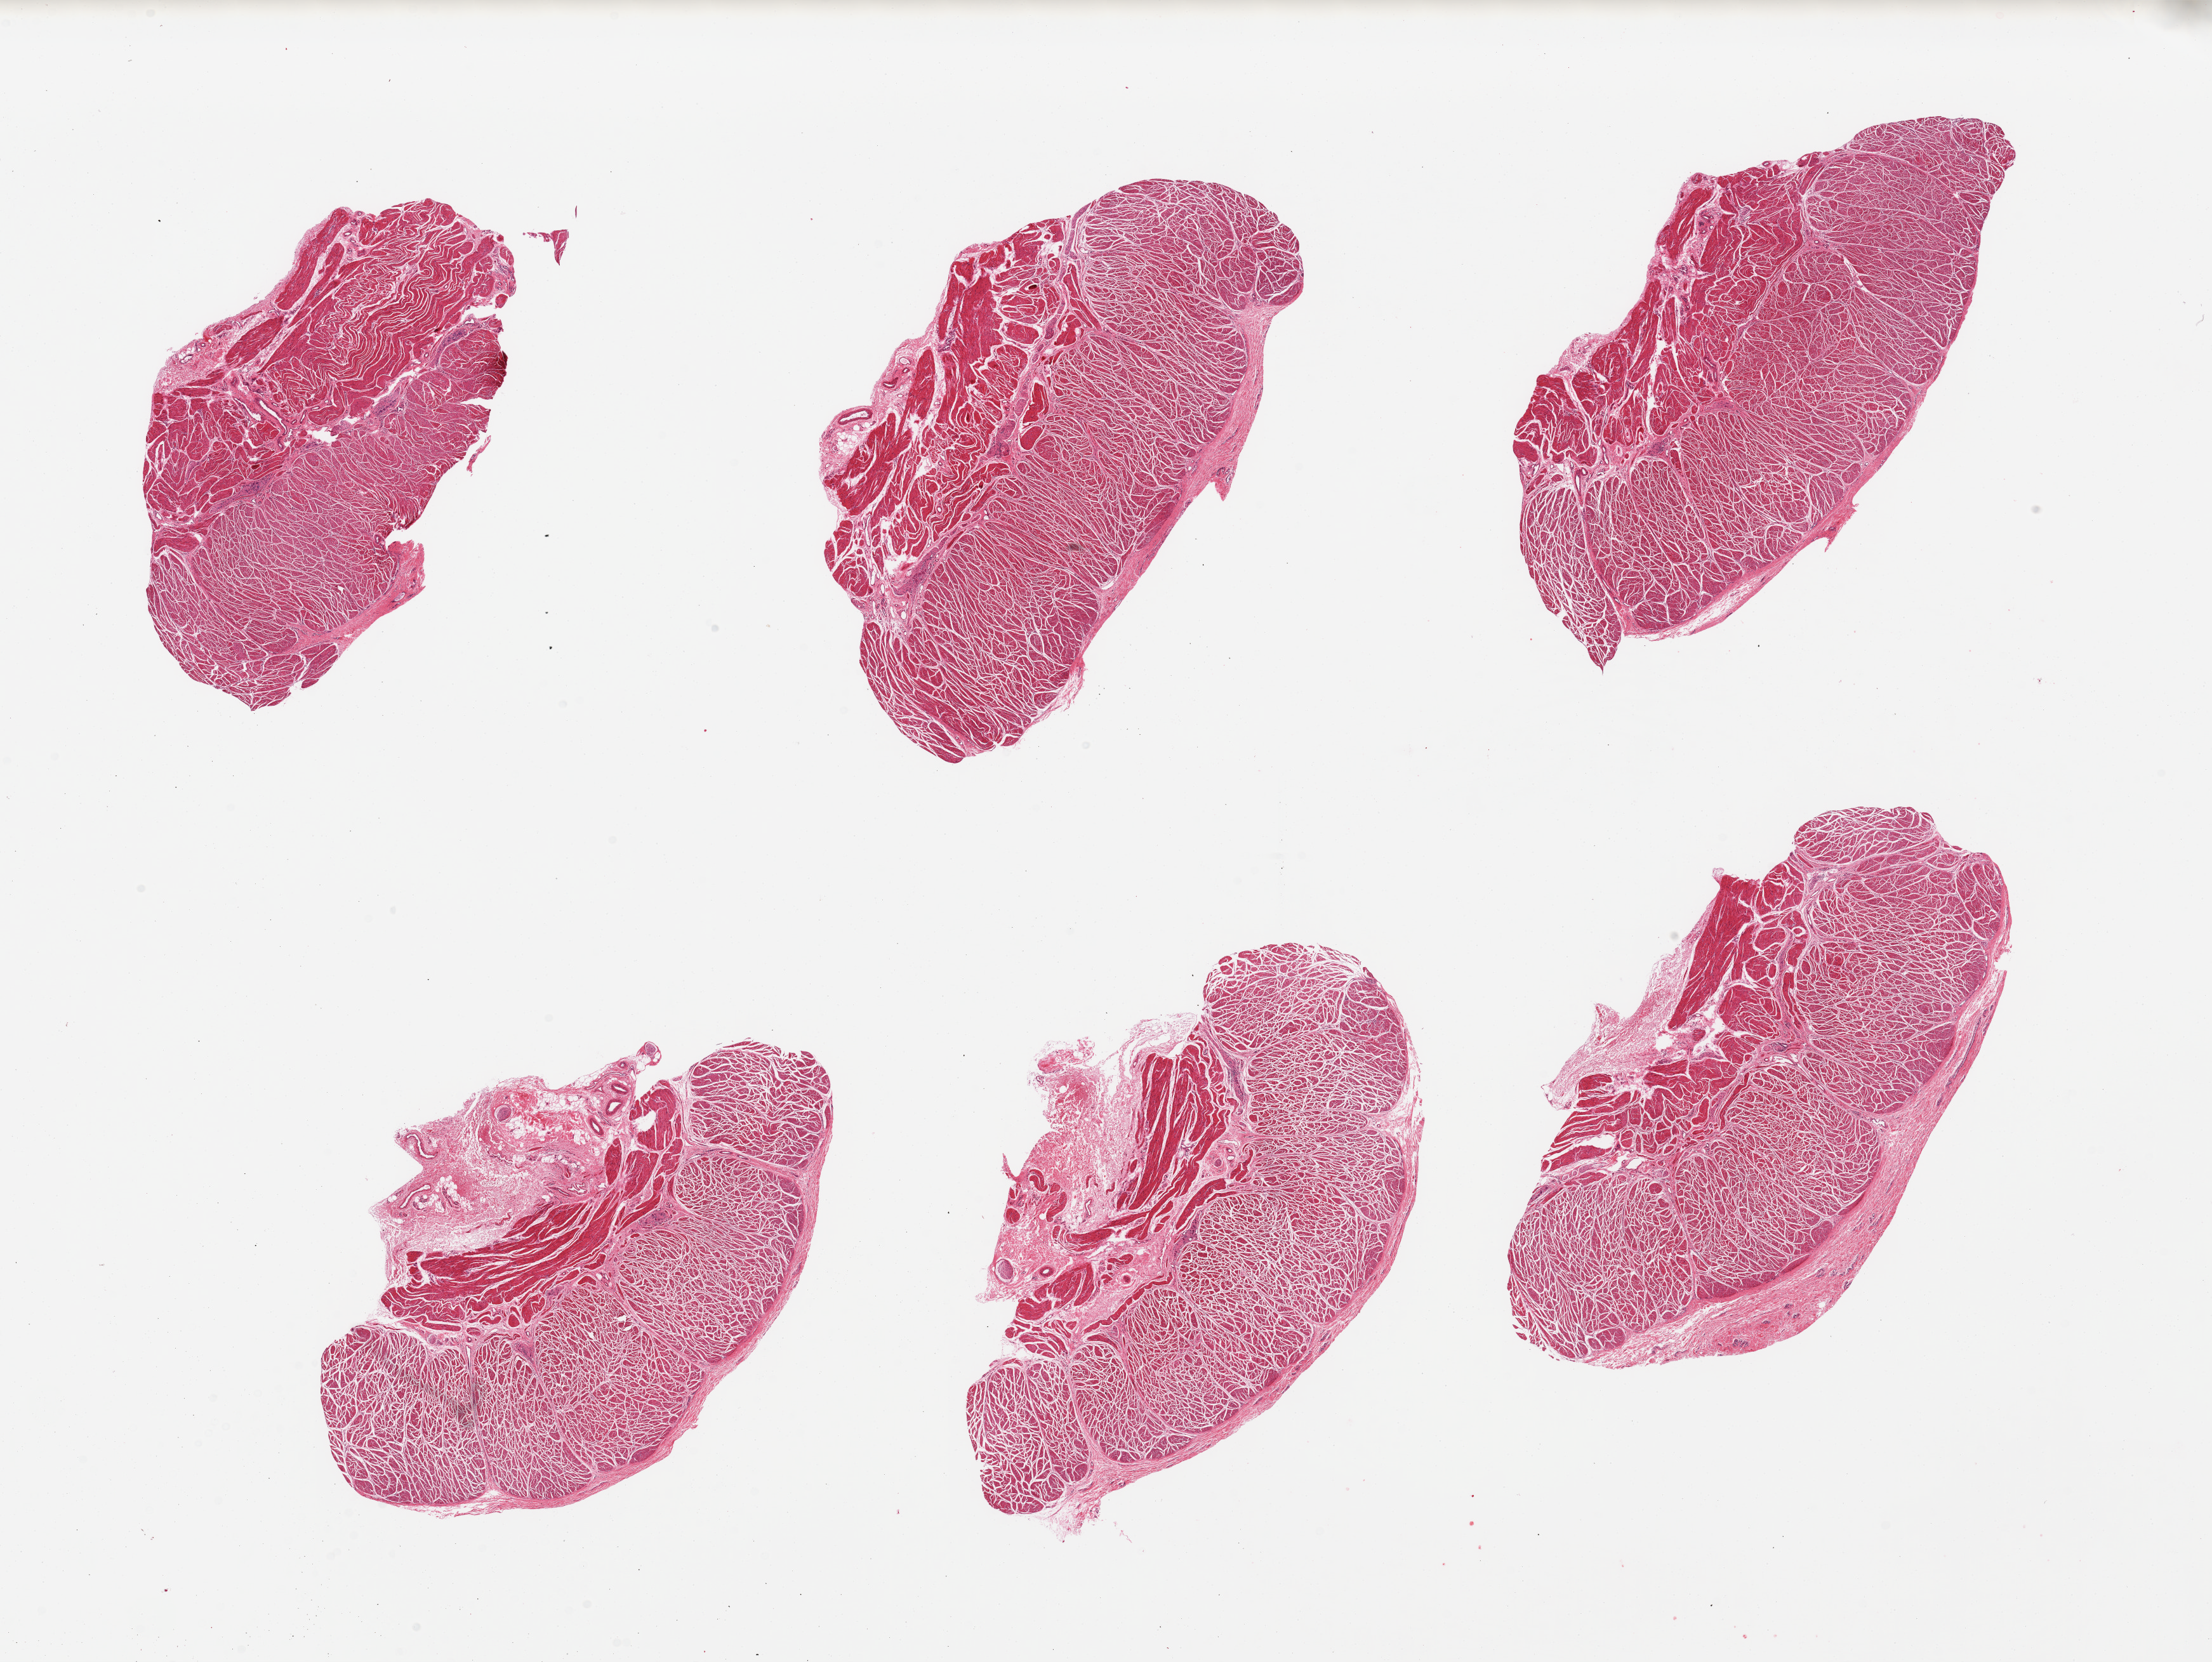
Haematoxylin and eosin whole-slide image, brightfield, a low-resolution overview of the entire scanned area, about 27.6 x 20.7 mm, PAXgene-fixed, paraffin-embedded tissue, target tissue: gastroesophageal junction, donor tissue sample. Donor sex: male.
Pathologist's review note for this sample: 6 pieces, all muscularis, focal connective tissue.